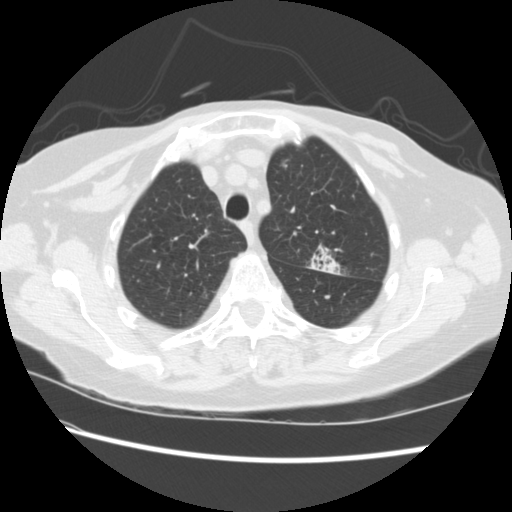
Axial slice from a low-dose chest CT screening exam. Baseline screening round. Lung window (W 1500 / L -600 HU). Standard (soft-tissue) reconstruction kernel (STANDARD). Slice 52 of 224 in the series. 512 × 512 image matrix, field of view 340 × 340 mm. Female, age 74 years at enrolment. Former smoker at enrolment.
Expert-annotated lung lesion, bounding box [x1, y1, x2, y2] px = [297, 239, 347, 281]. The screening reader recorded 2 non-calcified nodules or masses ≥4 mm on this exam (left upper lobe, right lower lobe); which of them this box marks is not recorded. Lung cancer was diagnosed 309 days after this screen: non-small cell carcinoma, left upper lobe, stage IV (AJCC 6th edition).